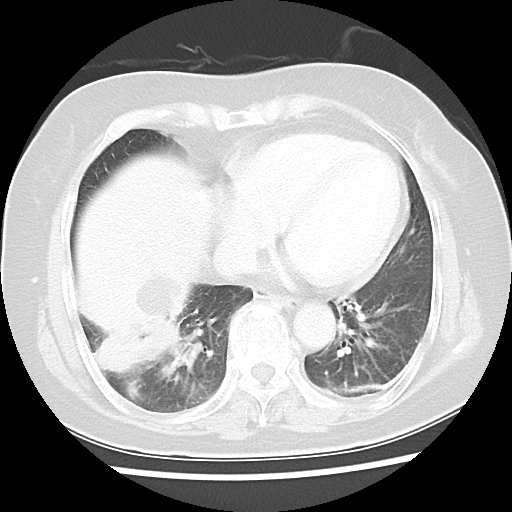
Chest CT, one axial slice; slice 14 of 45 in the series (ordered by position); 120 kVp; lung window (W 1500 / L -600 HU); 512 × 512 image matrix, field of view 312 × 312 mm. Patient: female, 65 years. Case-level facts recorded for this patient, not image findings: clinical TNM (as recorded): T2 N3 M0.
Structures marked on this image (rectangle marked by the reading radiologist):
- lung tumour (recorded histology: adenocarcinoma): box from (x=139, y=312) to (x=200, y=370) px